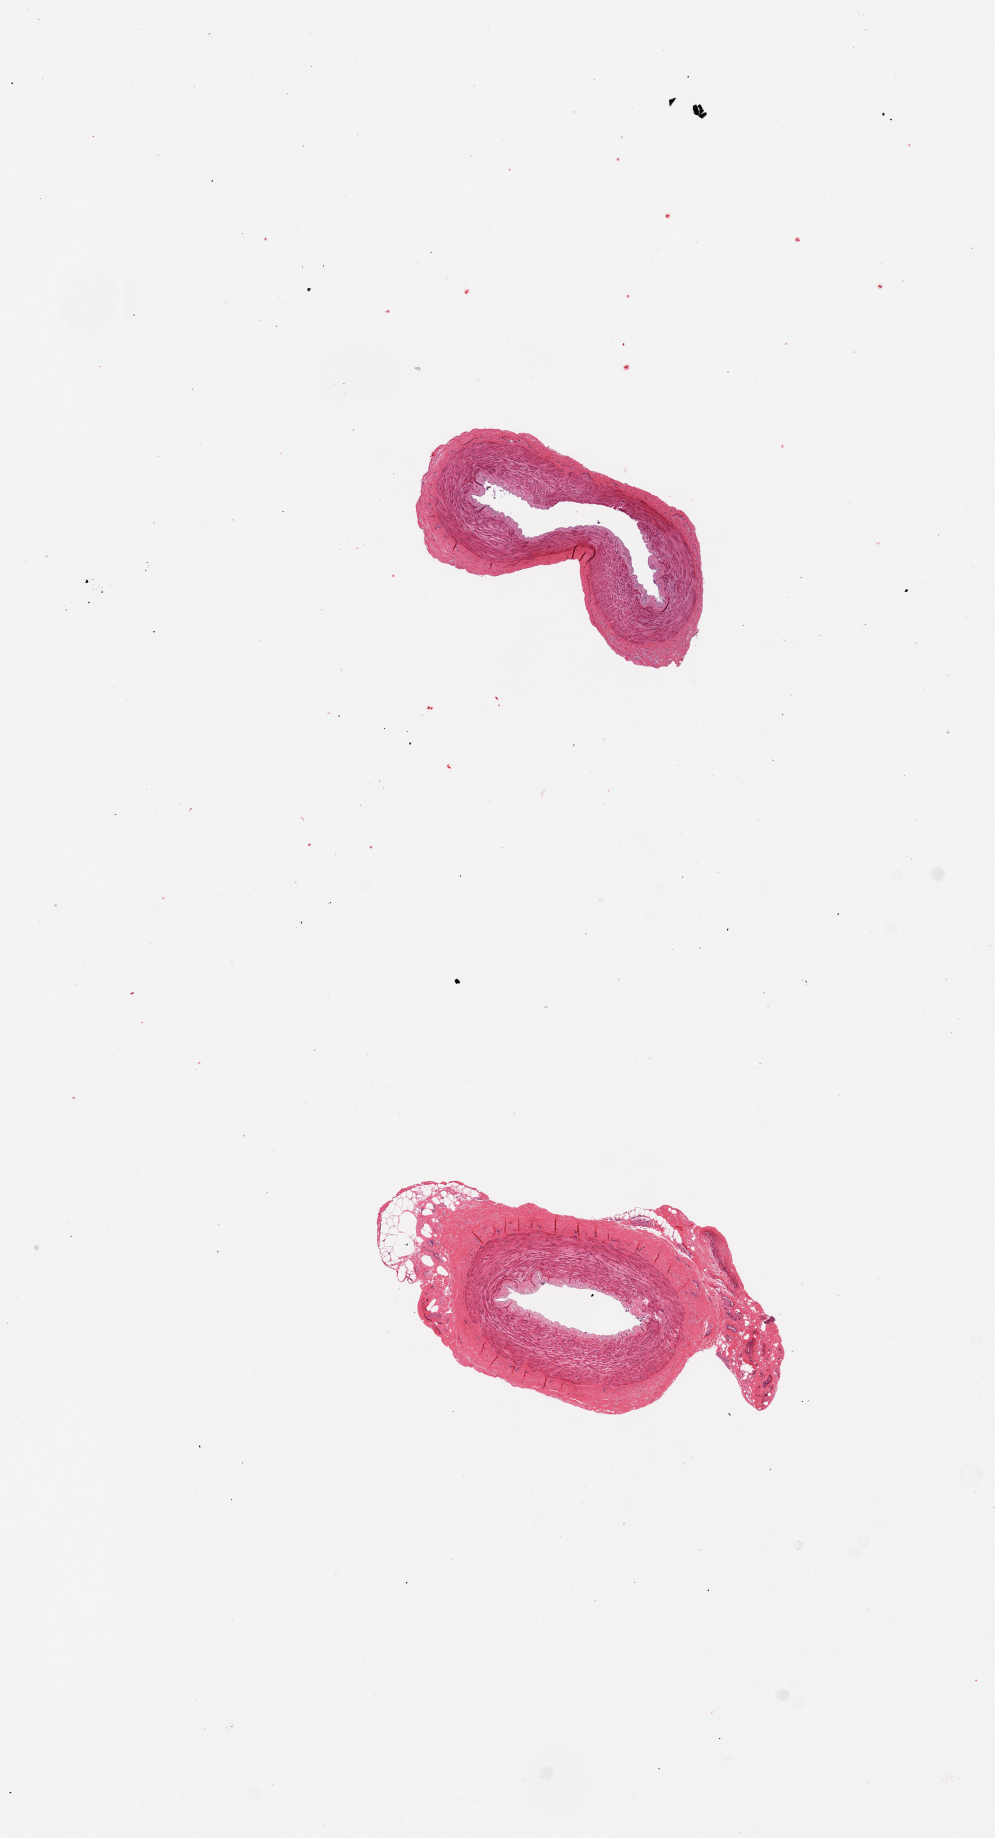
H&E whole-slide image, brightfield — a low-resolution overview of the entire scanned area, about 7.9 x 14.5 mm (slide scanned at 20x). PAXgene-fixed paraffin-embedded (PFPE) section. Target tissue: tibial artery. Tissue donor sample. Donor: male.
Pathologist's review note for this sample: 2 pieces. 30% external fat on one. No plaques.